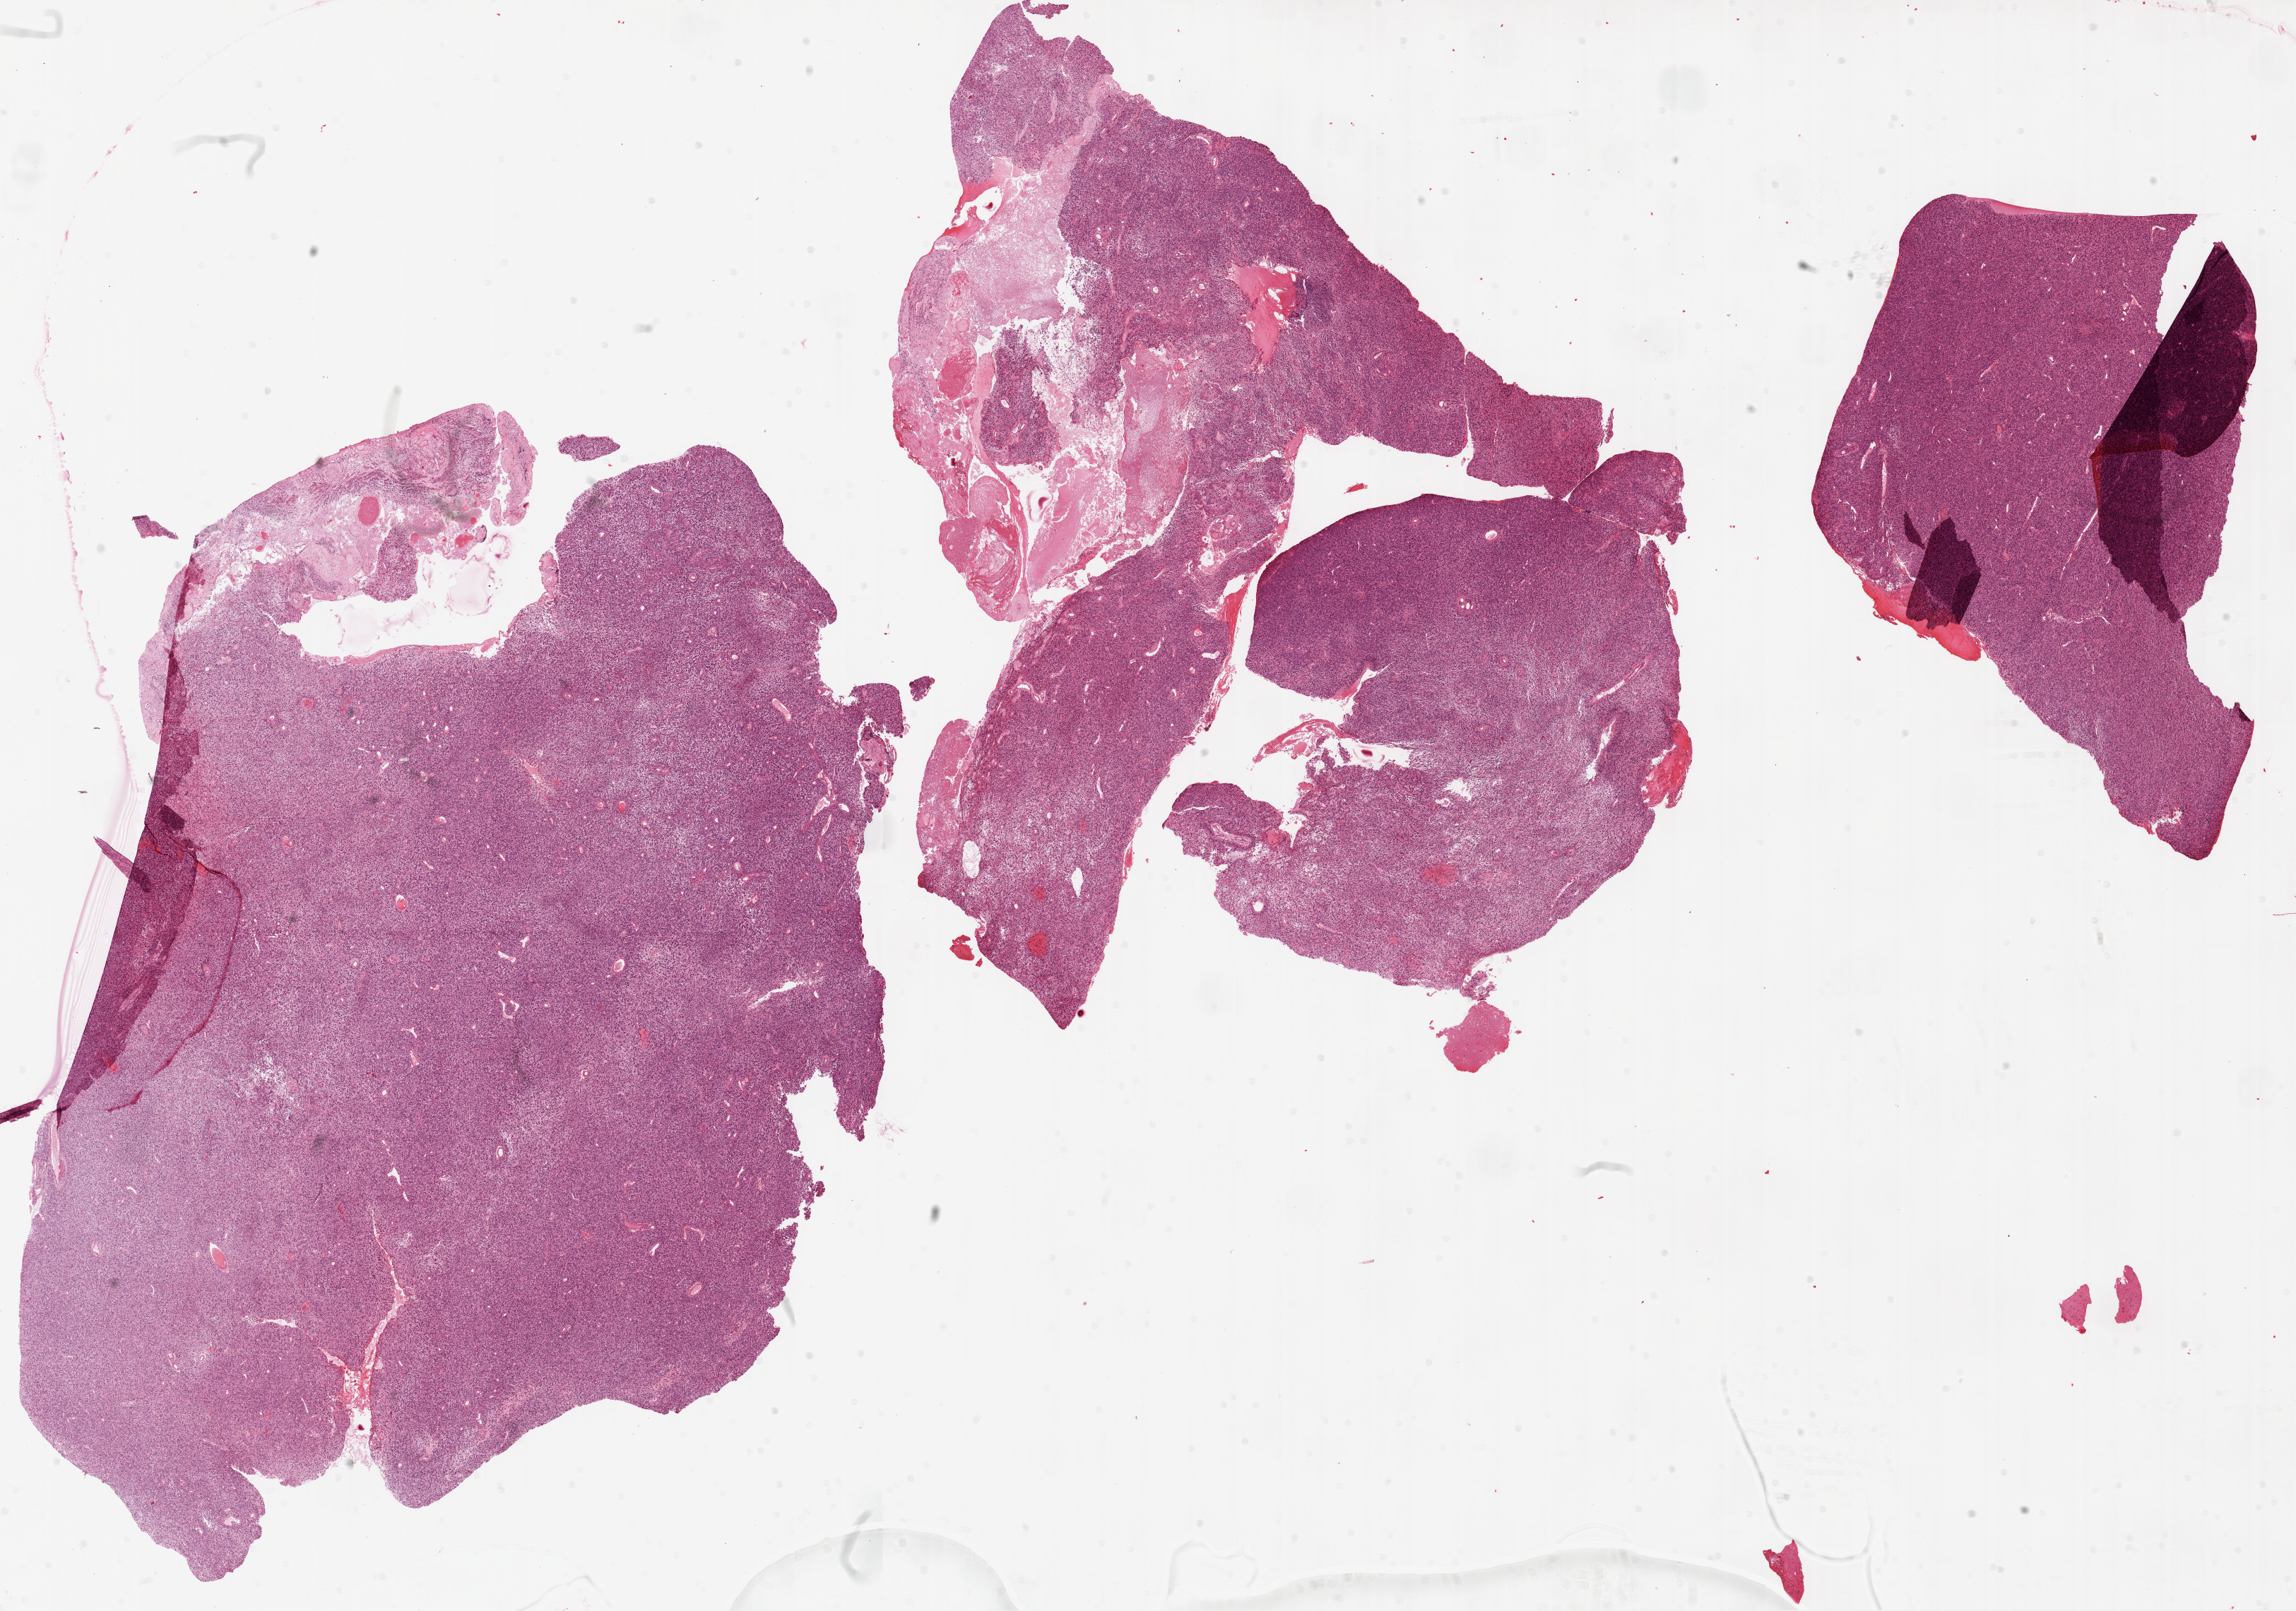
Digitized H&E tissue section (whole slide) — low-resolution overview of the scanned area, about 26.1 x 18.3 mm, formalin-fixed paraffin-embedded (FFPE) diagnostic section, primary tumour sample from the brain. Female, age 67 years at initial diagnosis.
Diagnosis: Glioblastoma.